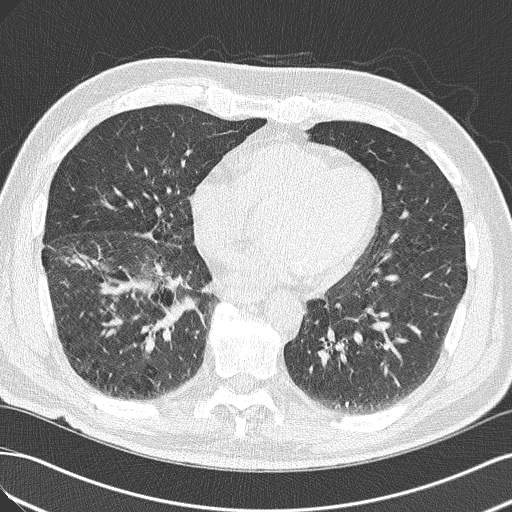
Axial slice from a low-dose chest CT screening exam, baseline annual screen, lung window (W 1500 / L -600 HU), 2 mm slice thickness, lung (sharp) reconstruction kernel (B50f), 512 × 512 image matrix, field of view 360 × 360 mm. Male participant, aged 65 years at enrolment. Current smoker at enrolment.
Lesion marked by an expert reader, bounding box [x1, y1, x2, y2] px = [103, 242, 202, 339]. The exam's reader record, not a measurement of the box and not confirmed to be the same lesion: non-calcified nodule or mass ≥4 mm, right upper lobe, 18 × 13 mm, spiculated (stellate) margins, soft tissue attenuation. Official screen result: positive, change unspecified: nodule(s) >= 4 mm or enlarging nodule(s), mass(es), or other non-specific abnormalities suspicious for lung cancer.